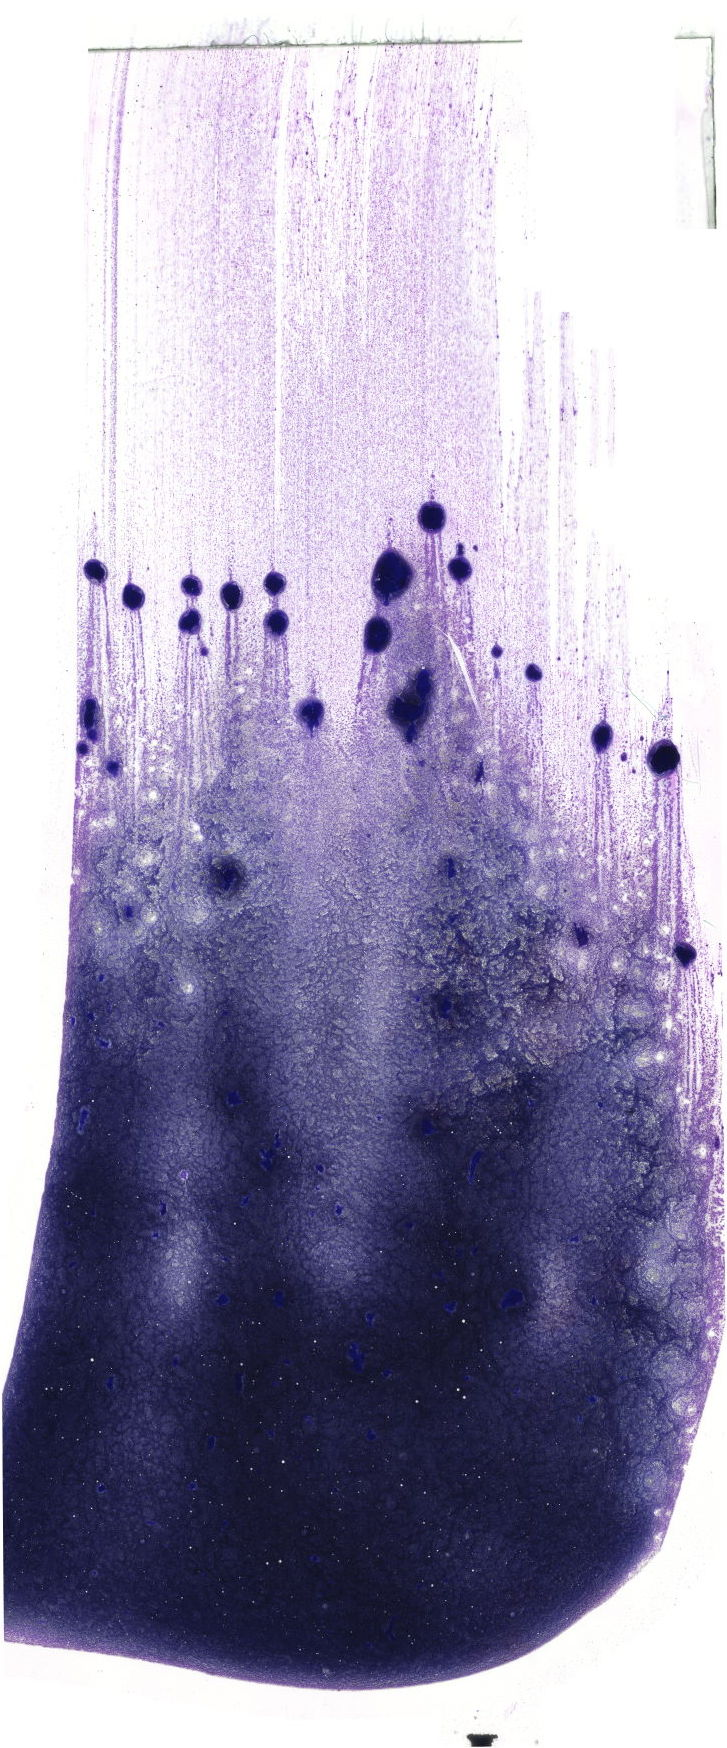
May-Grünwald-Giemsa (MGG)-stained marrow aspirate smear (whole slide) — shown as a low-resolution overview of the whole scanned area (about 20.6 x 49.5 mm). Male patient.
Diagnosis: Chronic Phase Chronic Myeloid Leukemia, BCR-ABL1 Positive.